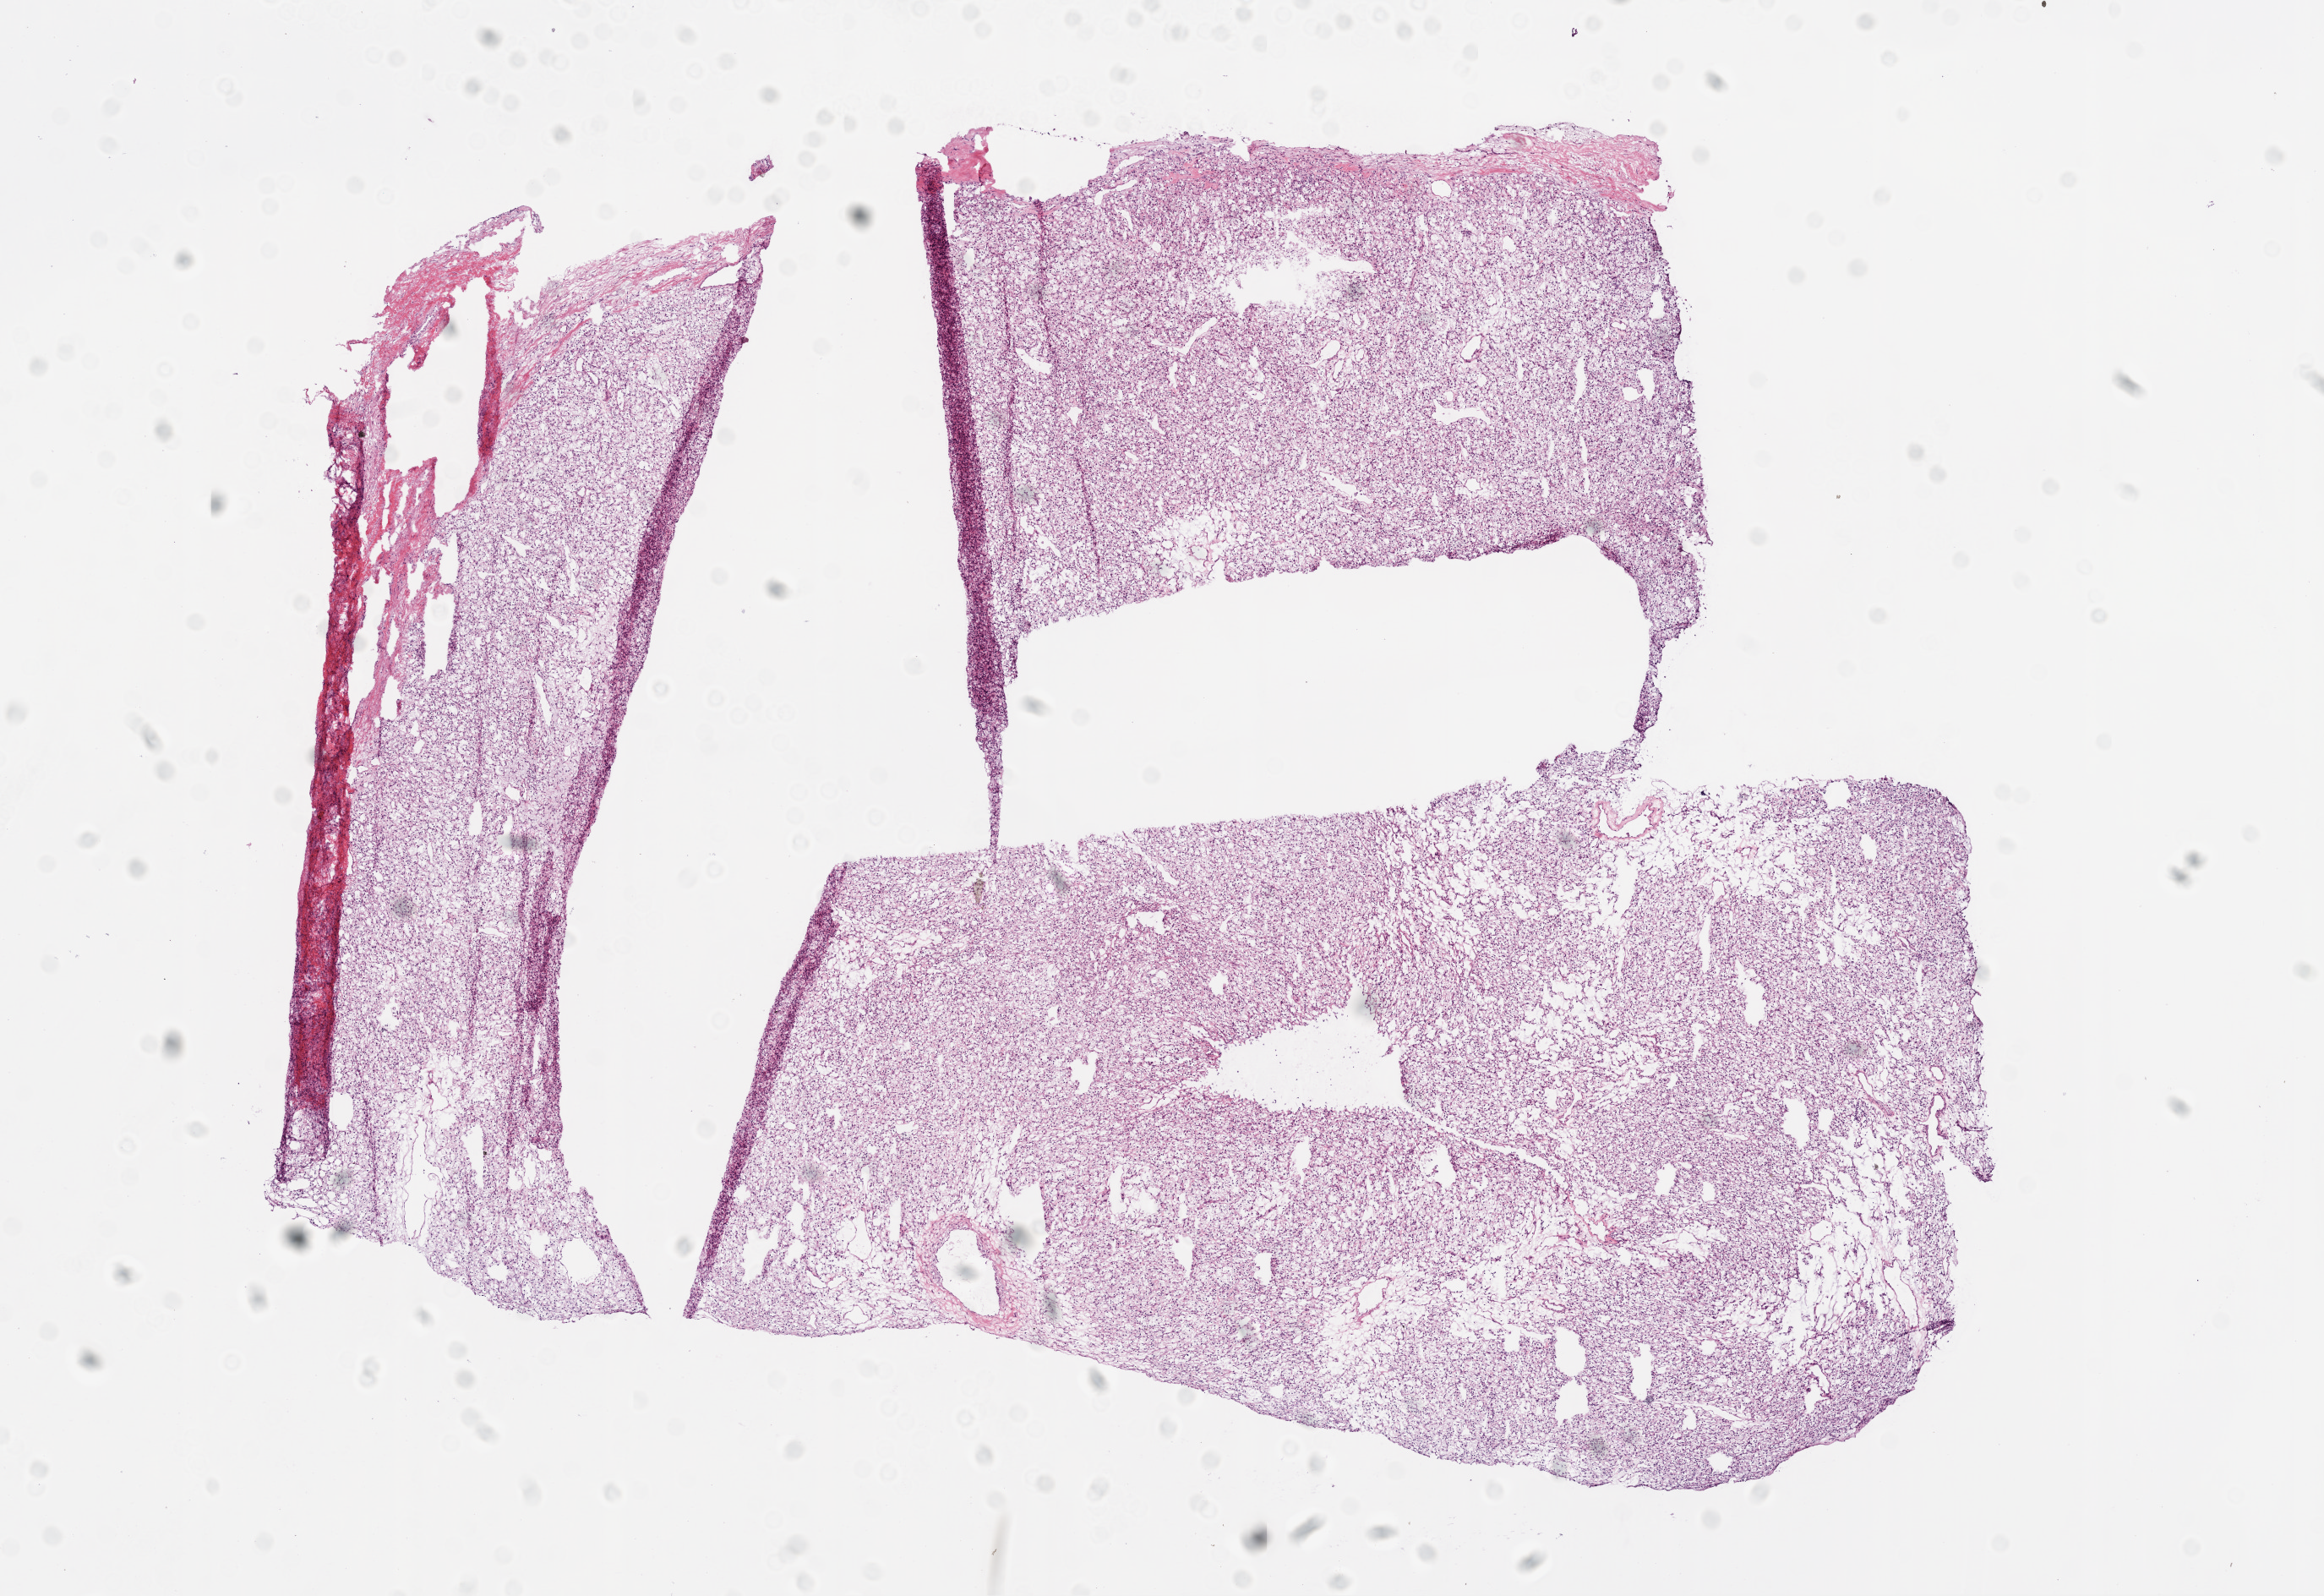
Digitized H&E-stained tissue section (whole slide) — shown as a low-resolution overview of the whole scanned area (about 11.0 x 7.6 mm, slide scanned at 20x), frozen section from the bottom of the tissue portion, kidney, primary tumour sample. Male, age 56 years at initial diagnosis. Histologic grade: G2 (moderately differentiated). Composition of this section per pathologist review: tumour cells 95%, tumour nuclei 85%, normal cells 0%, stromal cells 5%, necrosis 0%.
Laterality: left. Pathologic diagnosis: Clear cell adenocarcinoma, NOS. AJCC pathologic stage: I.